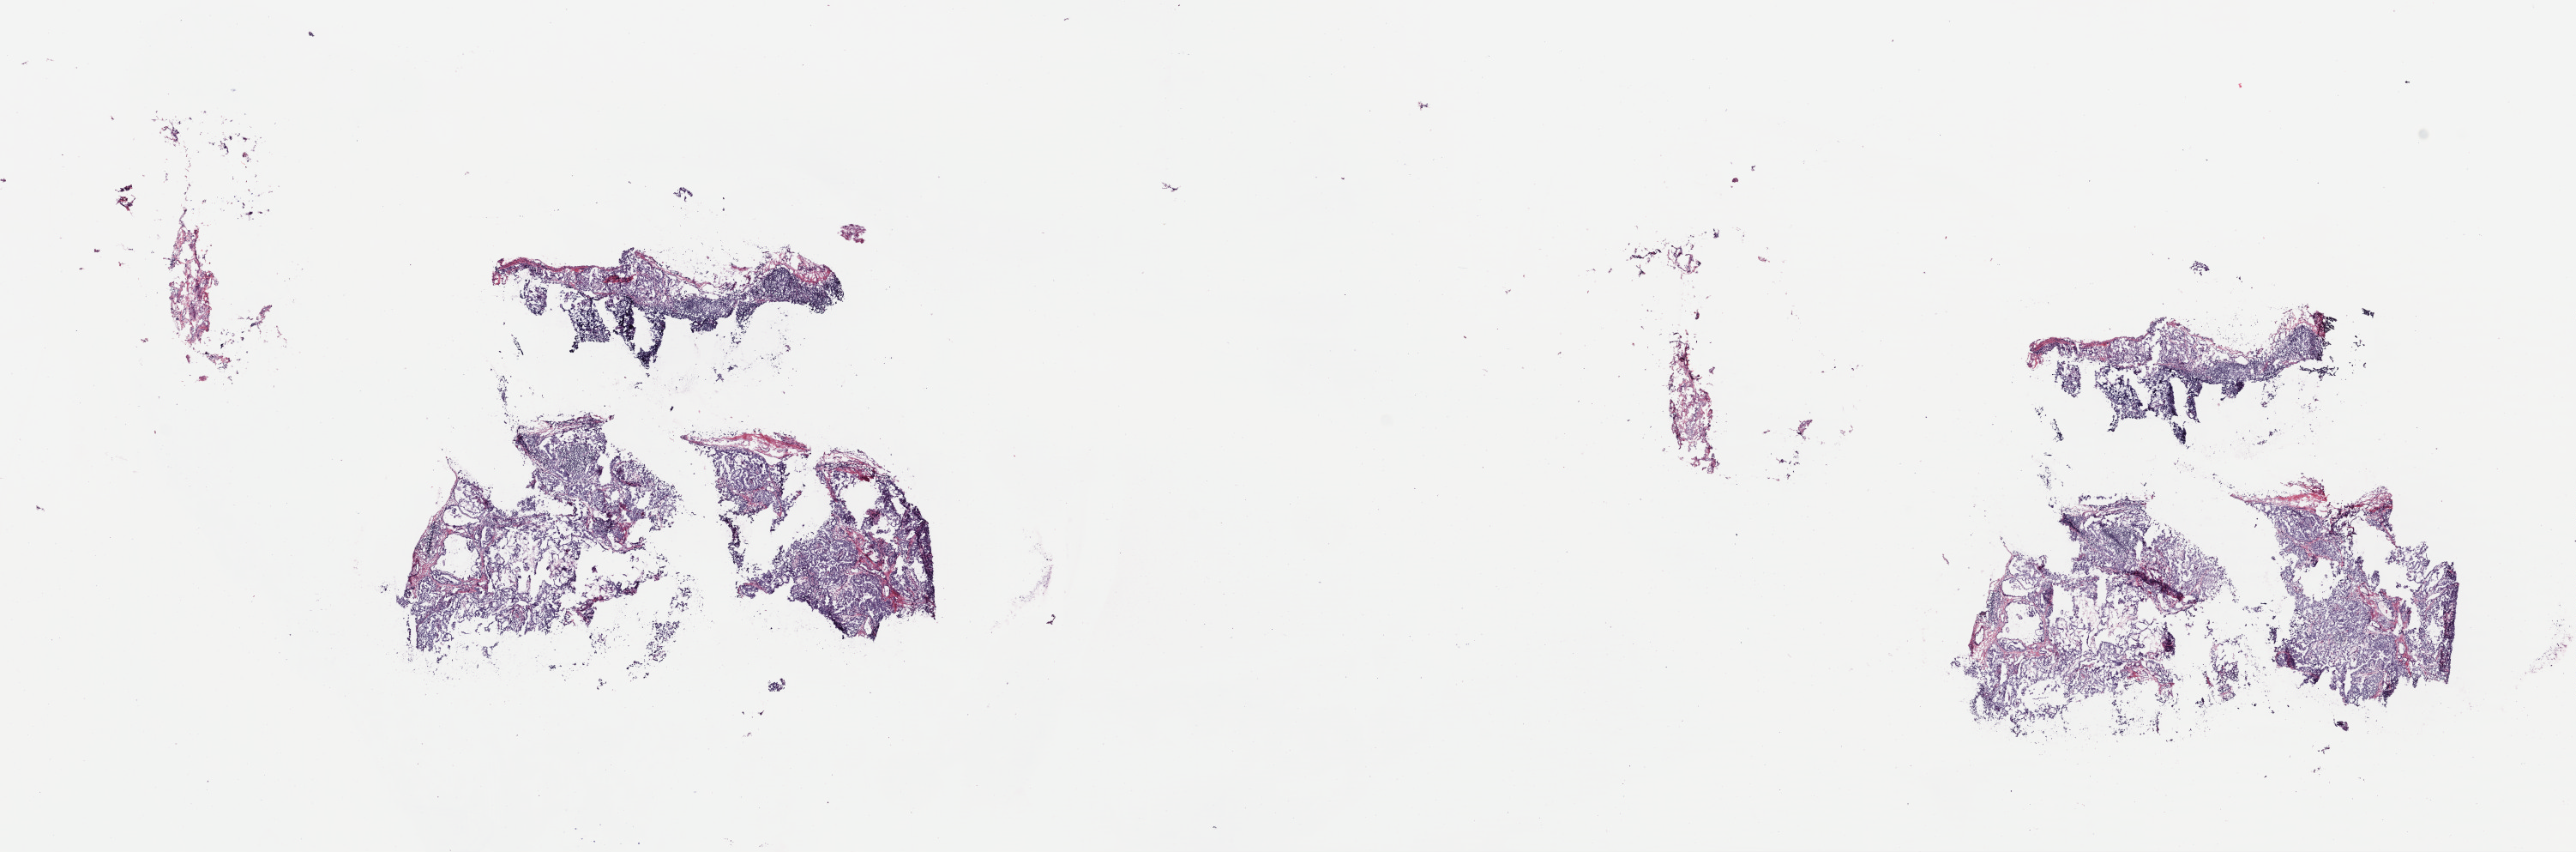
Whole-slide histology image, Hematoxylin and eosin (H&E) stained, shown as a low-resolution overview of the whole scanned area (about 23.6 x 7.8 mm, acquisition: 40x scan). Frozen section from the top of the tissue portion. Metastatic tumour sample, sampled site not recorded. Female patient; age at initial diagnosis 59 years. Composition of this section per pathologist review: tumour cells 30%, tumour nuclei 30%, normal cells 65%, stromal cells 5%, necrosis 0%. Inflammatory infiltration, as recorded: lymphocyte infiltration 30%, monocyte infiltration 0%, neutrophil infiltration 0%.
• this section: metastatic tumour tissue
• patient diagnosis: Papillary adenocarcinoma, NOS (primary site: thyroid gland)